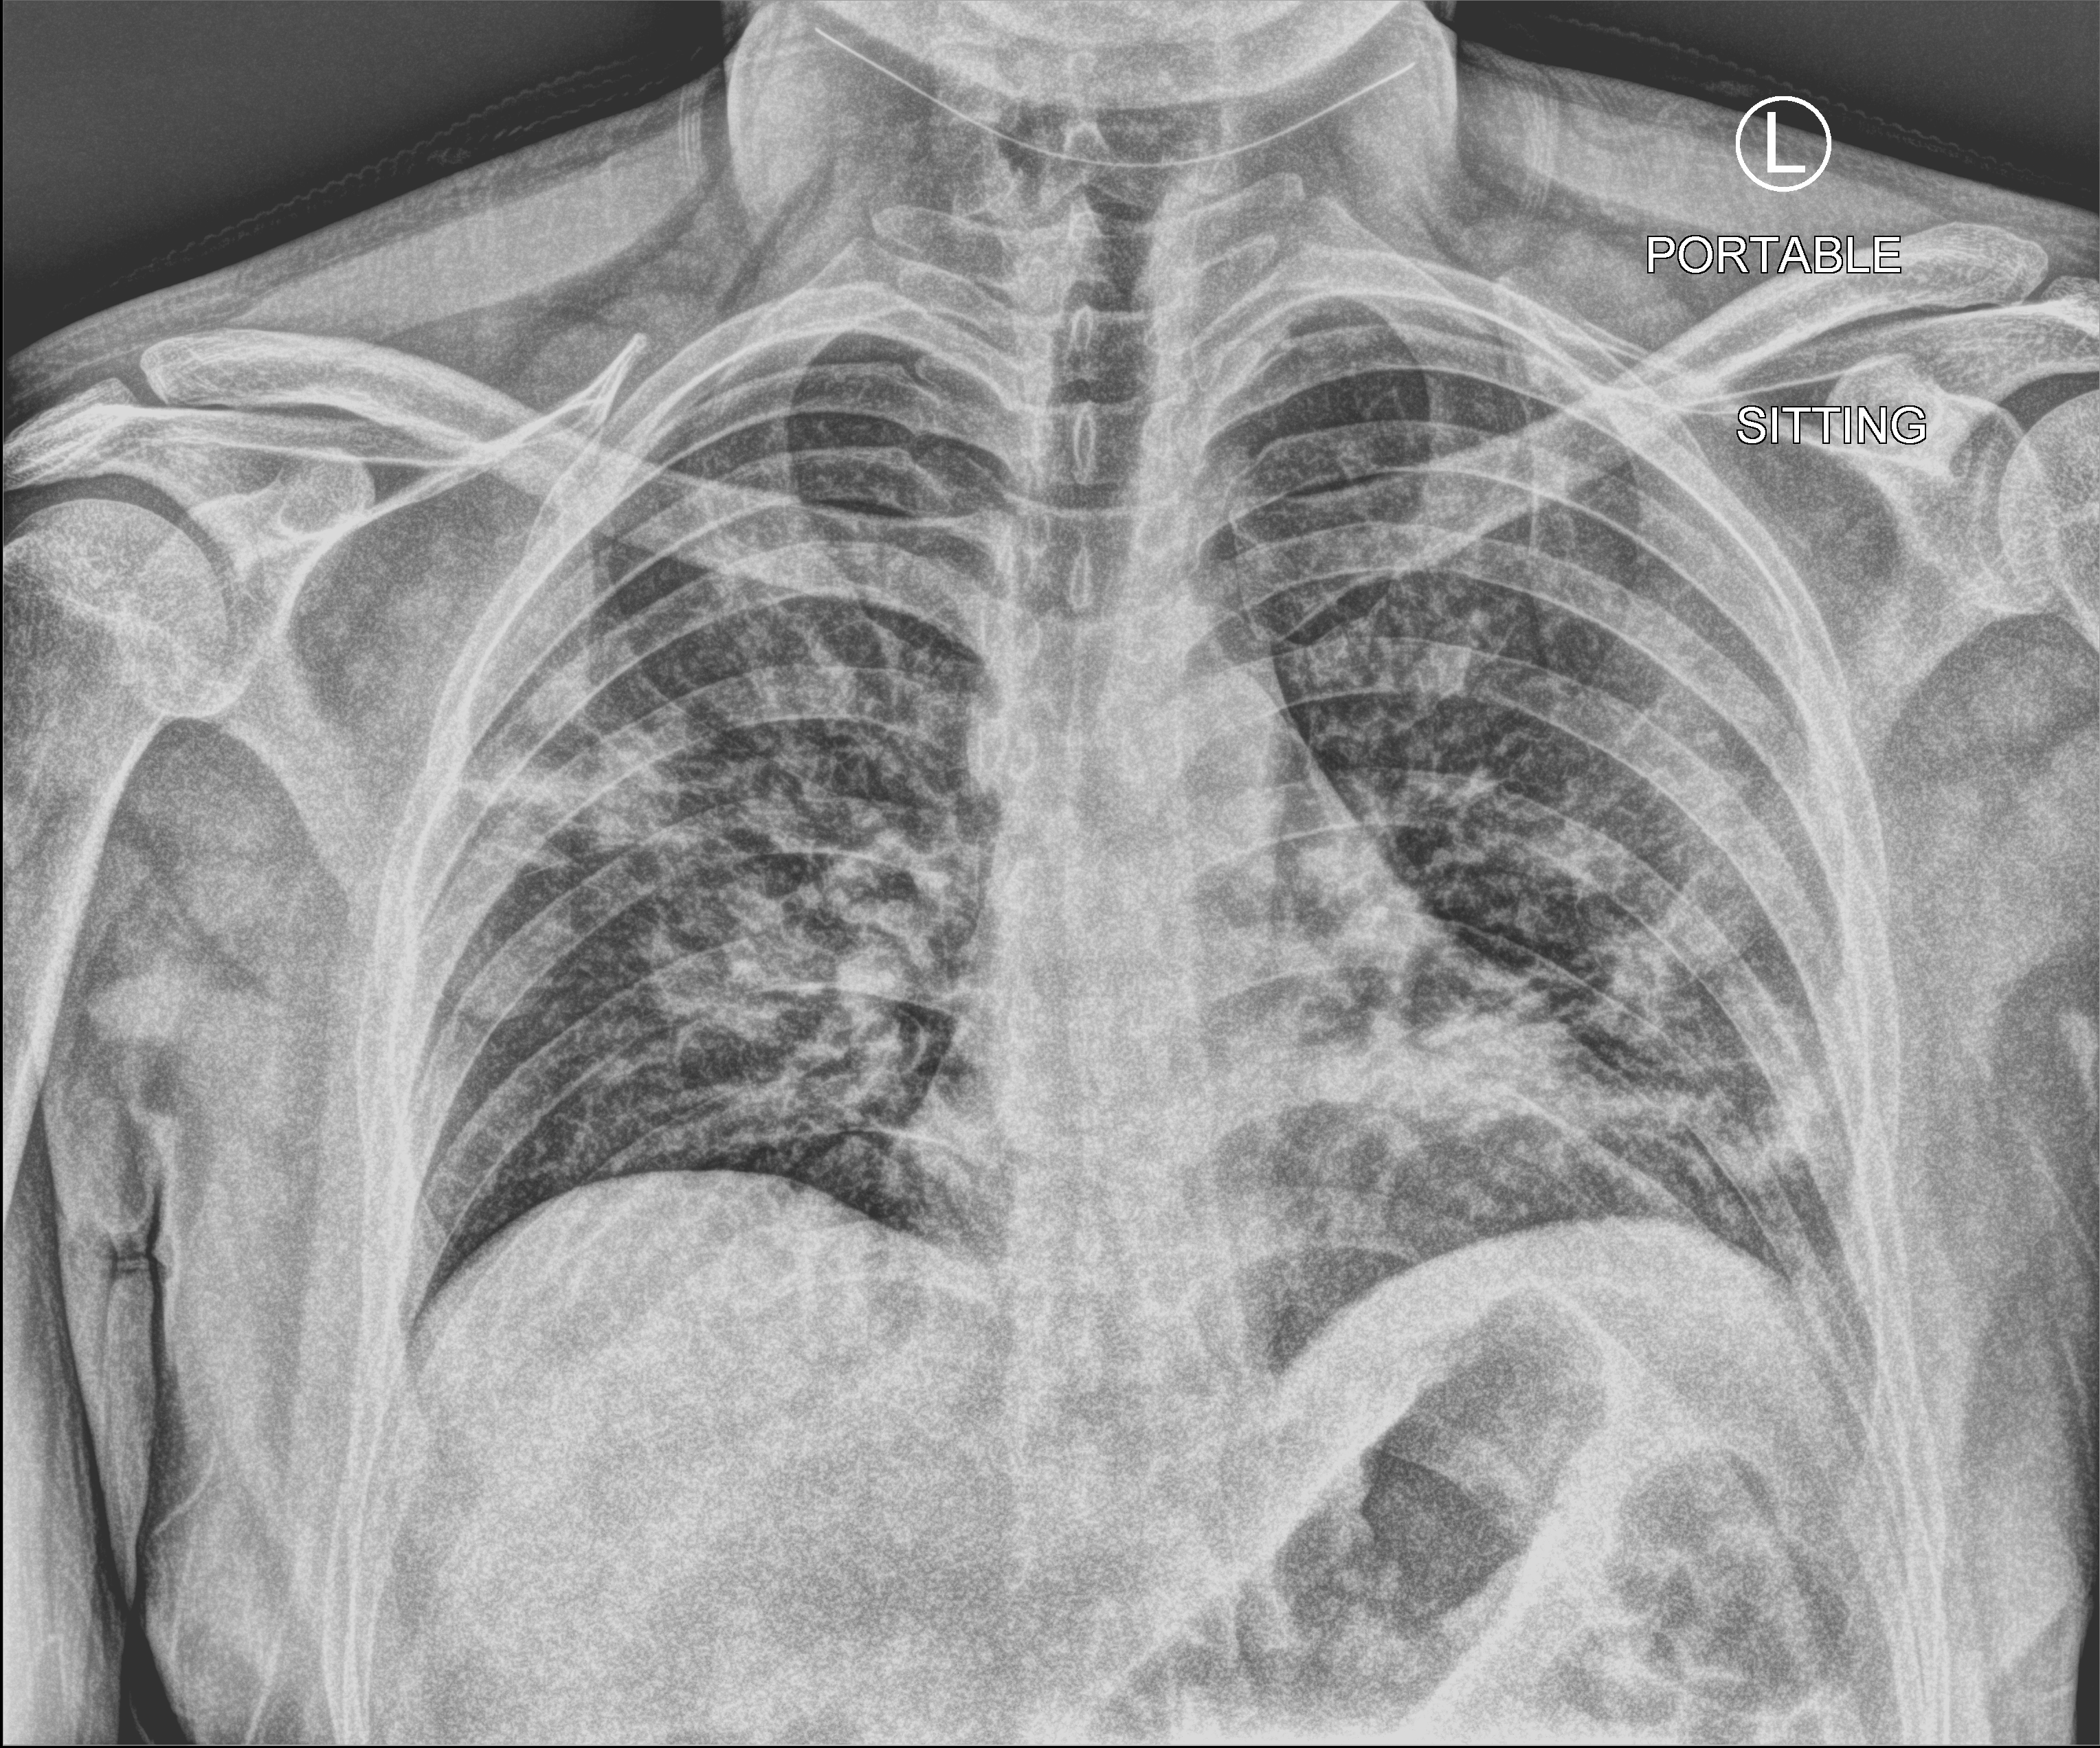
Bedside chest radiograph (computed radiography). Male patient hospitalised with COVID-19, age 18–59 years.
Admission-level facts for this patient (not findings on this image; timing relative to this image not recorded): COPD (admission record): no; admitted to intensive care during this hospital stay: no.